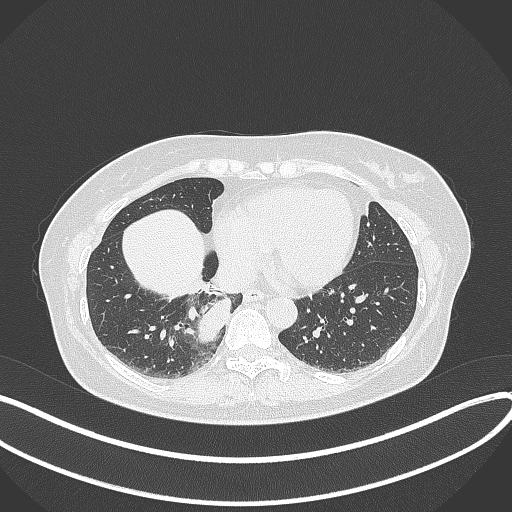
Chest CT, one axial slice; position 111 of 331 along the scan axis; reconstruction kernel B70f; 120 kVp; lung window (W 1500 / L -600 HU); 1 mm slice thickness; 512 × 512 image matrix, field of view 400 × 400 mm. Patient: female, 54 years. Case-level facts recorded for this patient, not image findings: clinical TNM (as recorded): T4 N0 M0.
Structures marked on this image (bounding box drawn by a radiologist):
- lung tumour (recorded histology: adenocarcinoma): bounding box [x1, y1, x2, y2] px = [191, 289, 239, 352]